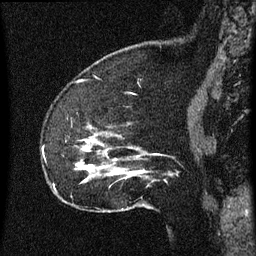
Breast MRI (dynamic contrast-enhanced), one sagittal slice. Position 15 of 60 along the scan axis. Dynamic contrast-enhanced series, image 2 of 3 at this slice position (ordered by acquisition). 1.5 T. TE 4.2 ms, TR 8 ms. 256 × 256 image matrix. Patient: female, 52 years.
Structures marked on this image (semi-automatically segmented with operator editing):
- analysis volume of interest (the breast-tissue region the enhancement analysis was run in; not a lesion): box from (x=54, y=120) to (x=168, y=207) px
- tumour enhancement mask (voxels above the 70 % enhancement threshold inside the analysis volume of interest): (x=77, y=148)–(x=157, y=173)